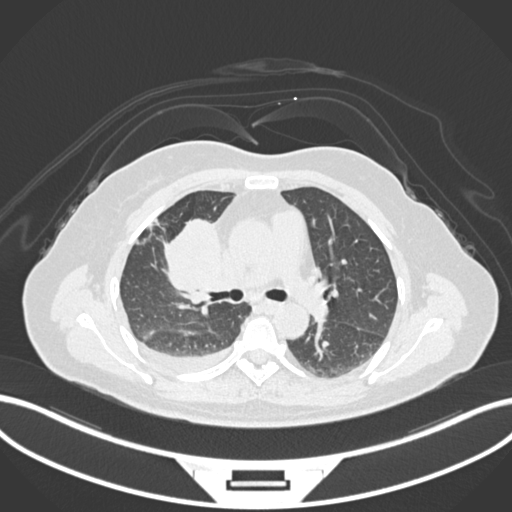
Chest CT, one axial slice; position 89 of 172 along the scan axis; 120 kVp; lung window (W 1500 / L -600 HU); 512 × 512 image matrix, field of view 400 × 400 mm. Patient: female, 52 years. From the clinical record (not read from this slice): clinical TNM (as recorded): T3 N1 M1.
Annotated regions visible in this slice (rectangle marked by the reading radiologist):
- lung tumour (recorded histology: adenocarcinoma): bounding box <163,216,225,304> (left, top, right, bottom; pixels)